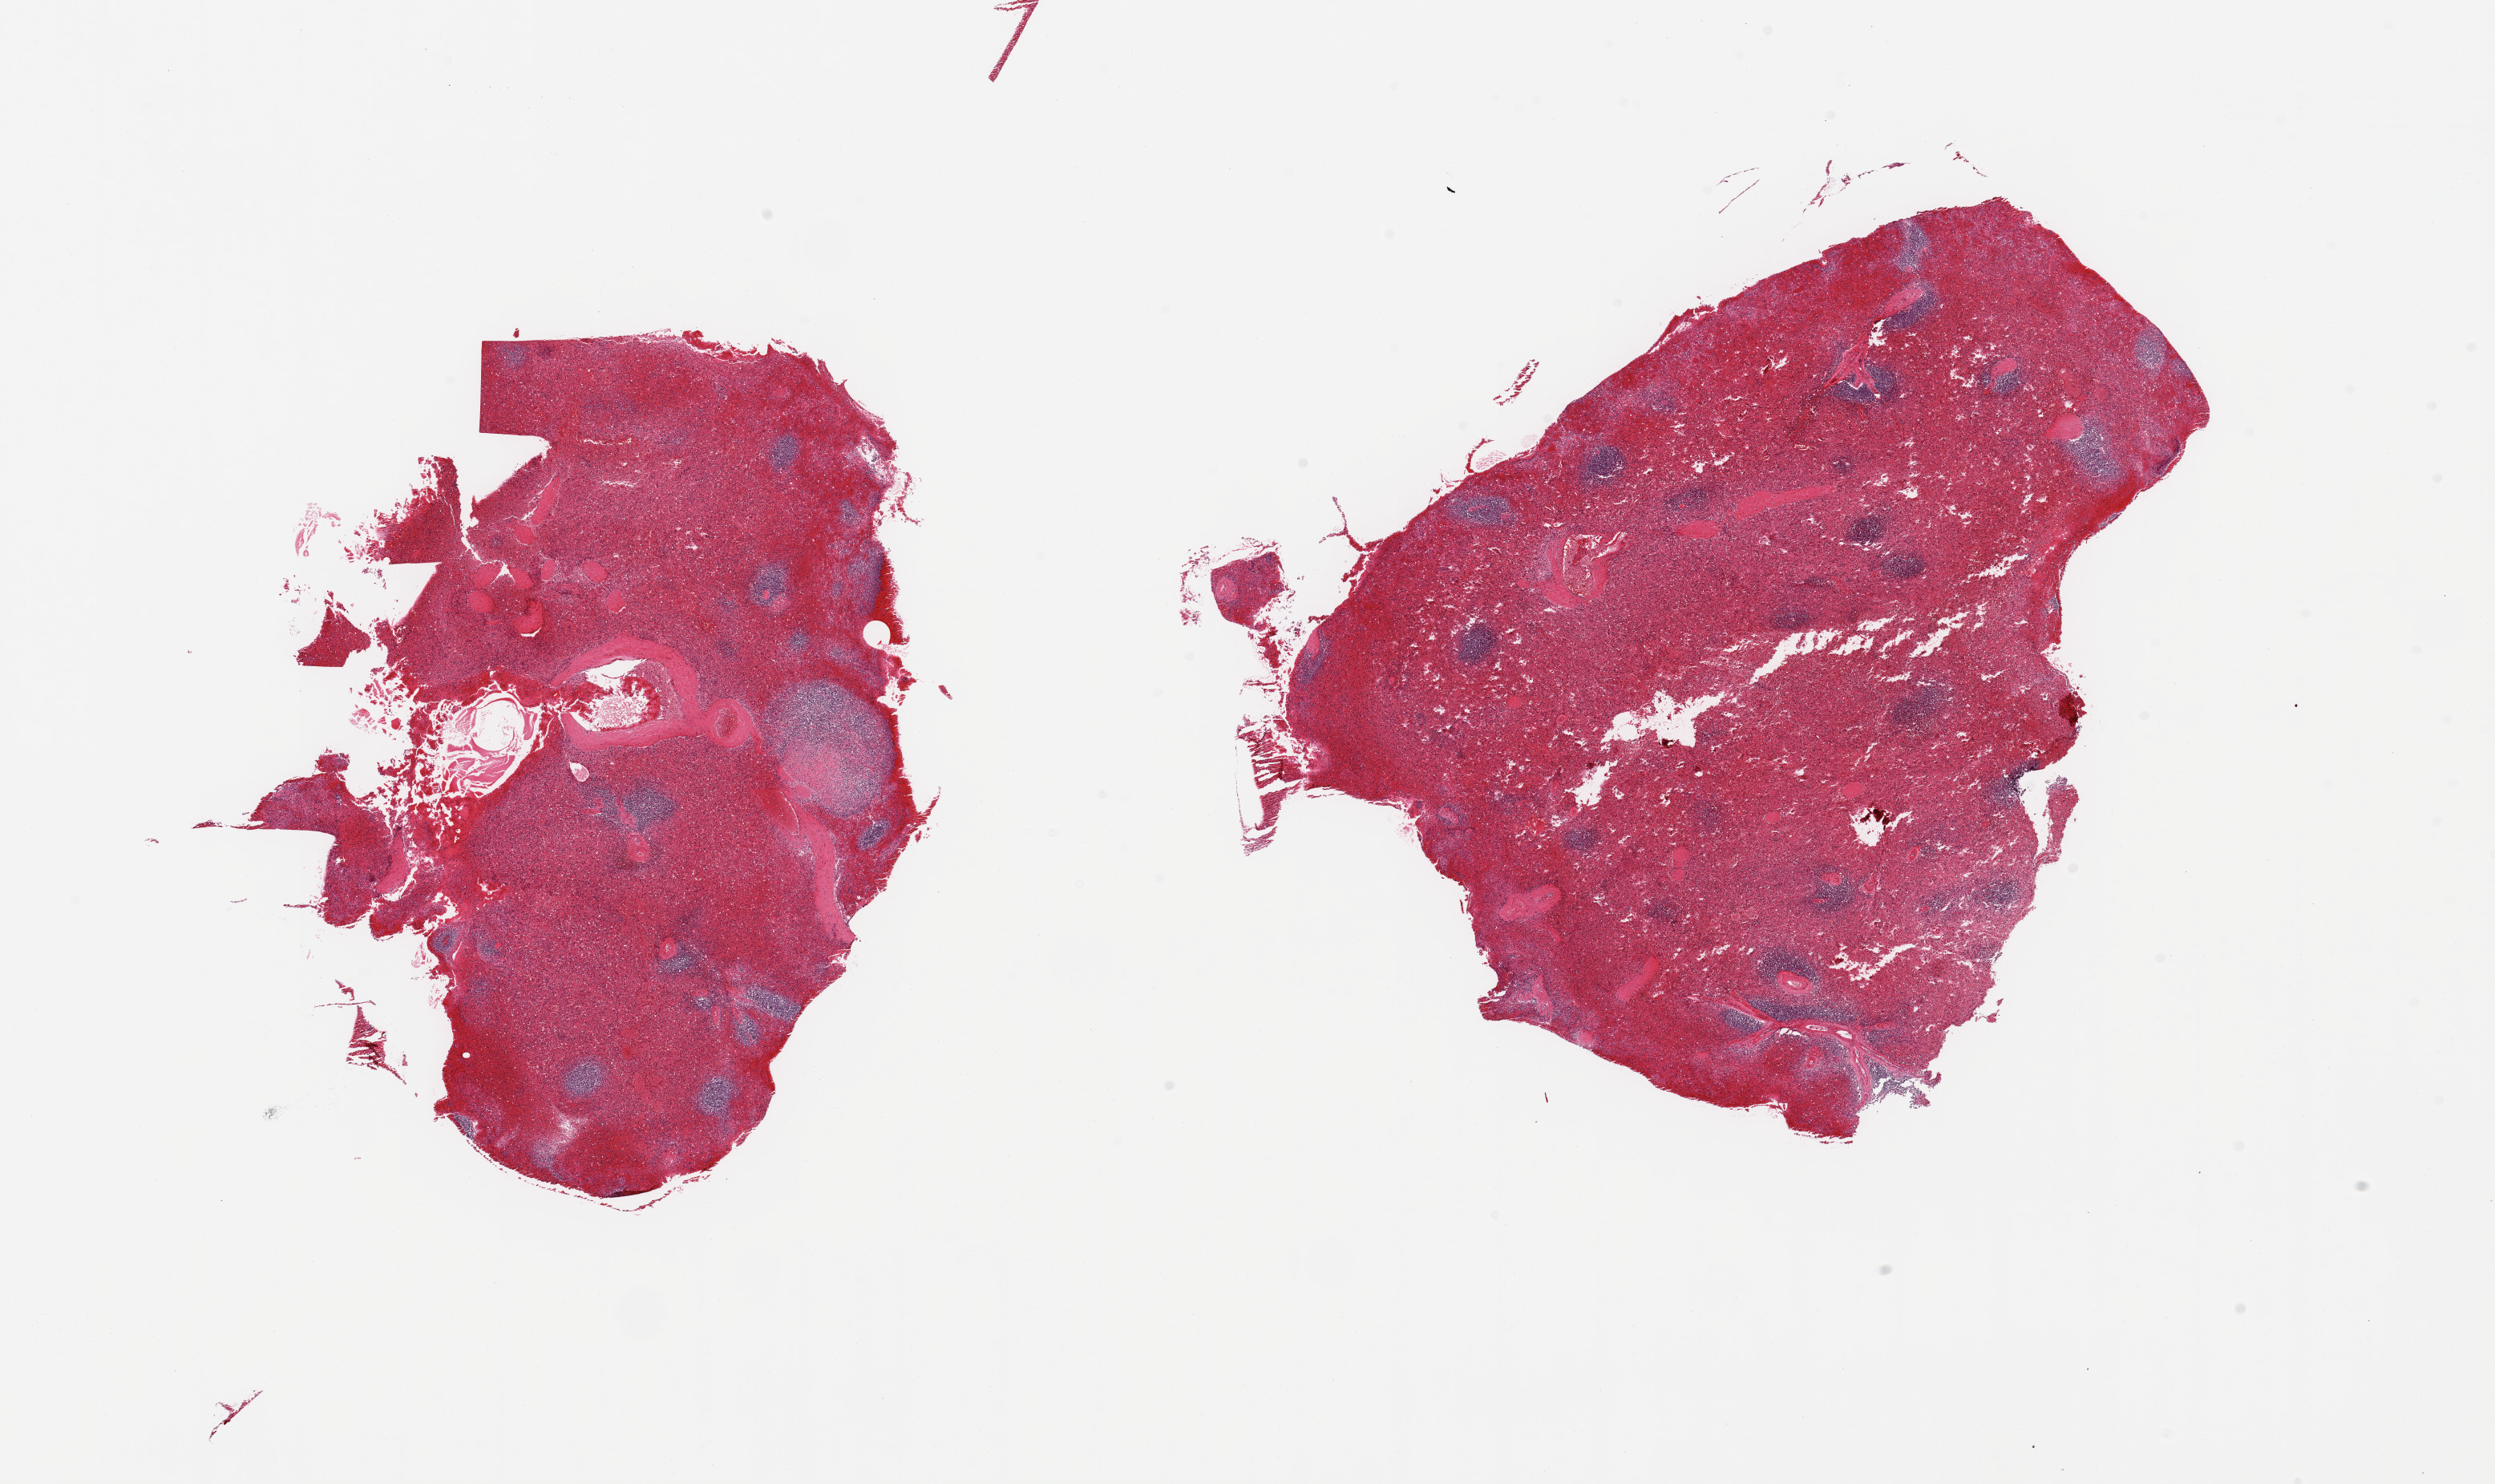
Hematoxylin and eosin (H&E) whole-slide image — a low-resolution overview of the entire scanned area, about 24.6 x 14.6 mm, PAXgene-fixed paraffin-embedded (PFPE) section, sampled site (target tissue): spleen, tissue donor sample. Male donor.
Pathologist's review note for this sample: 2 pieces; marked congestion.